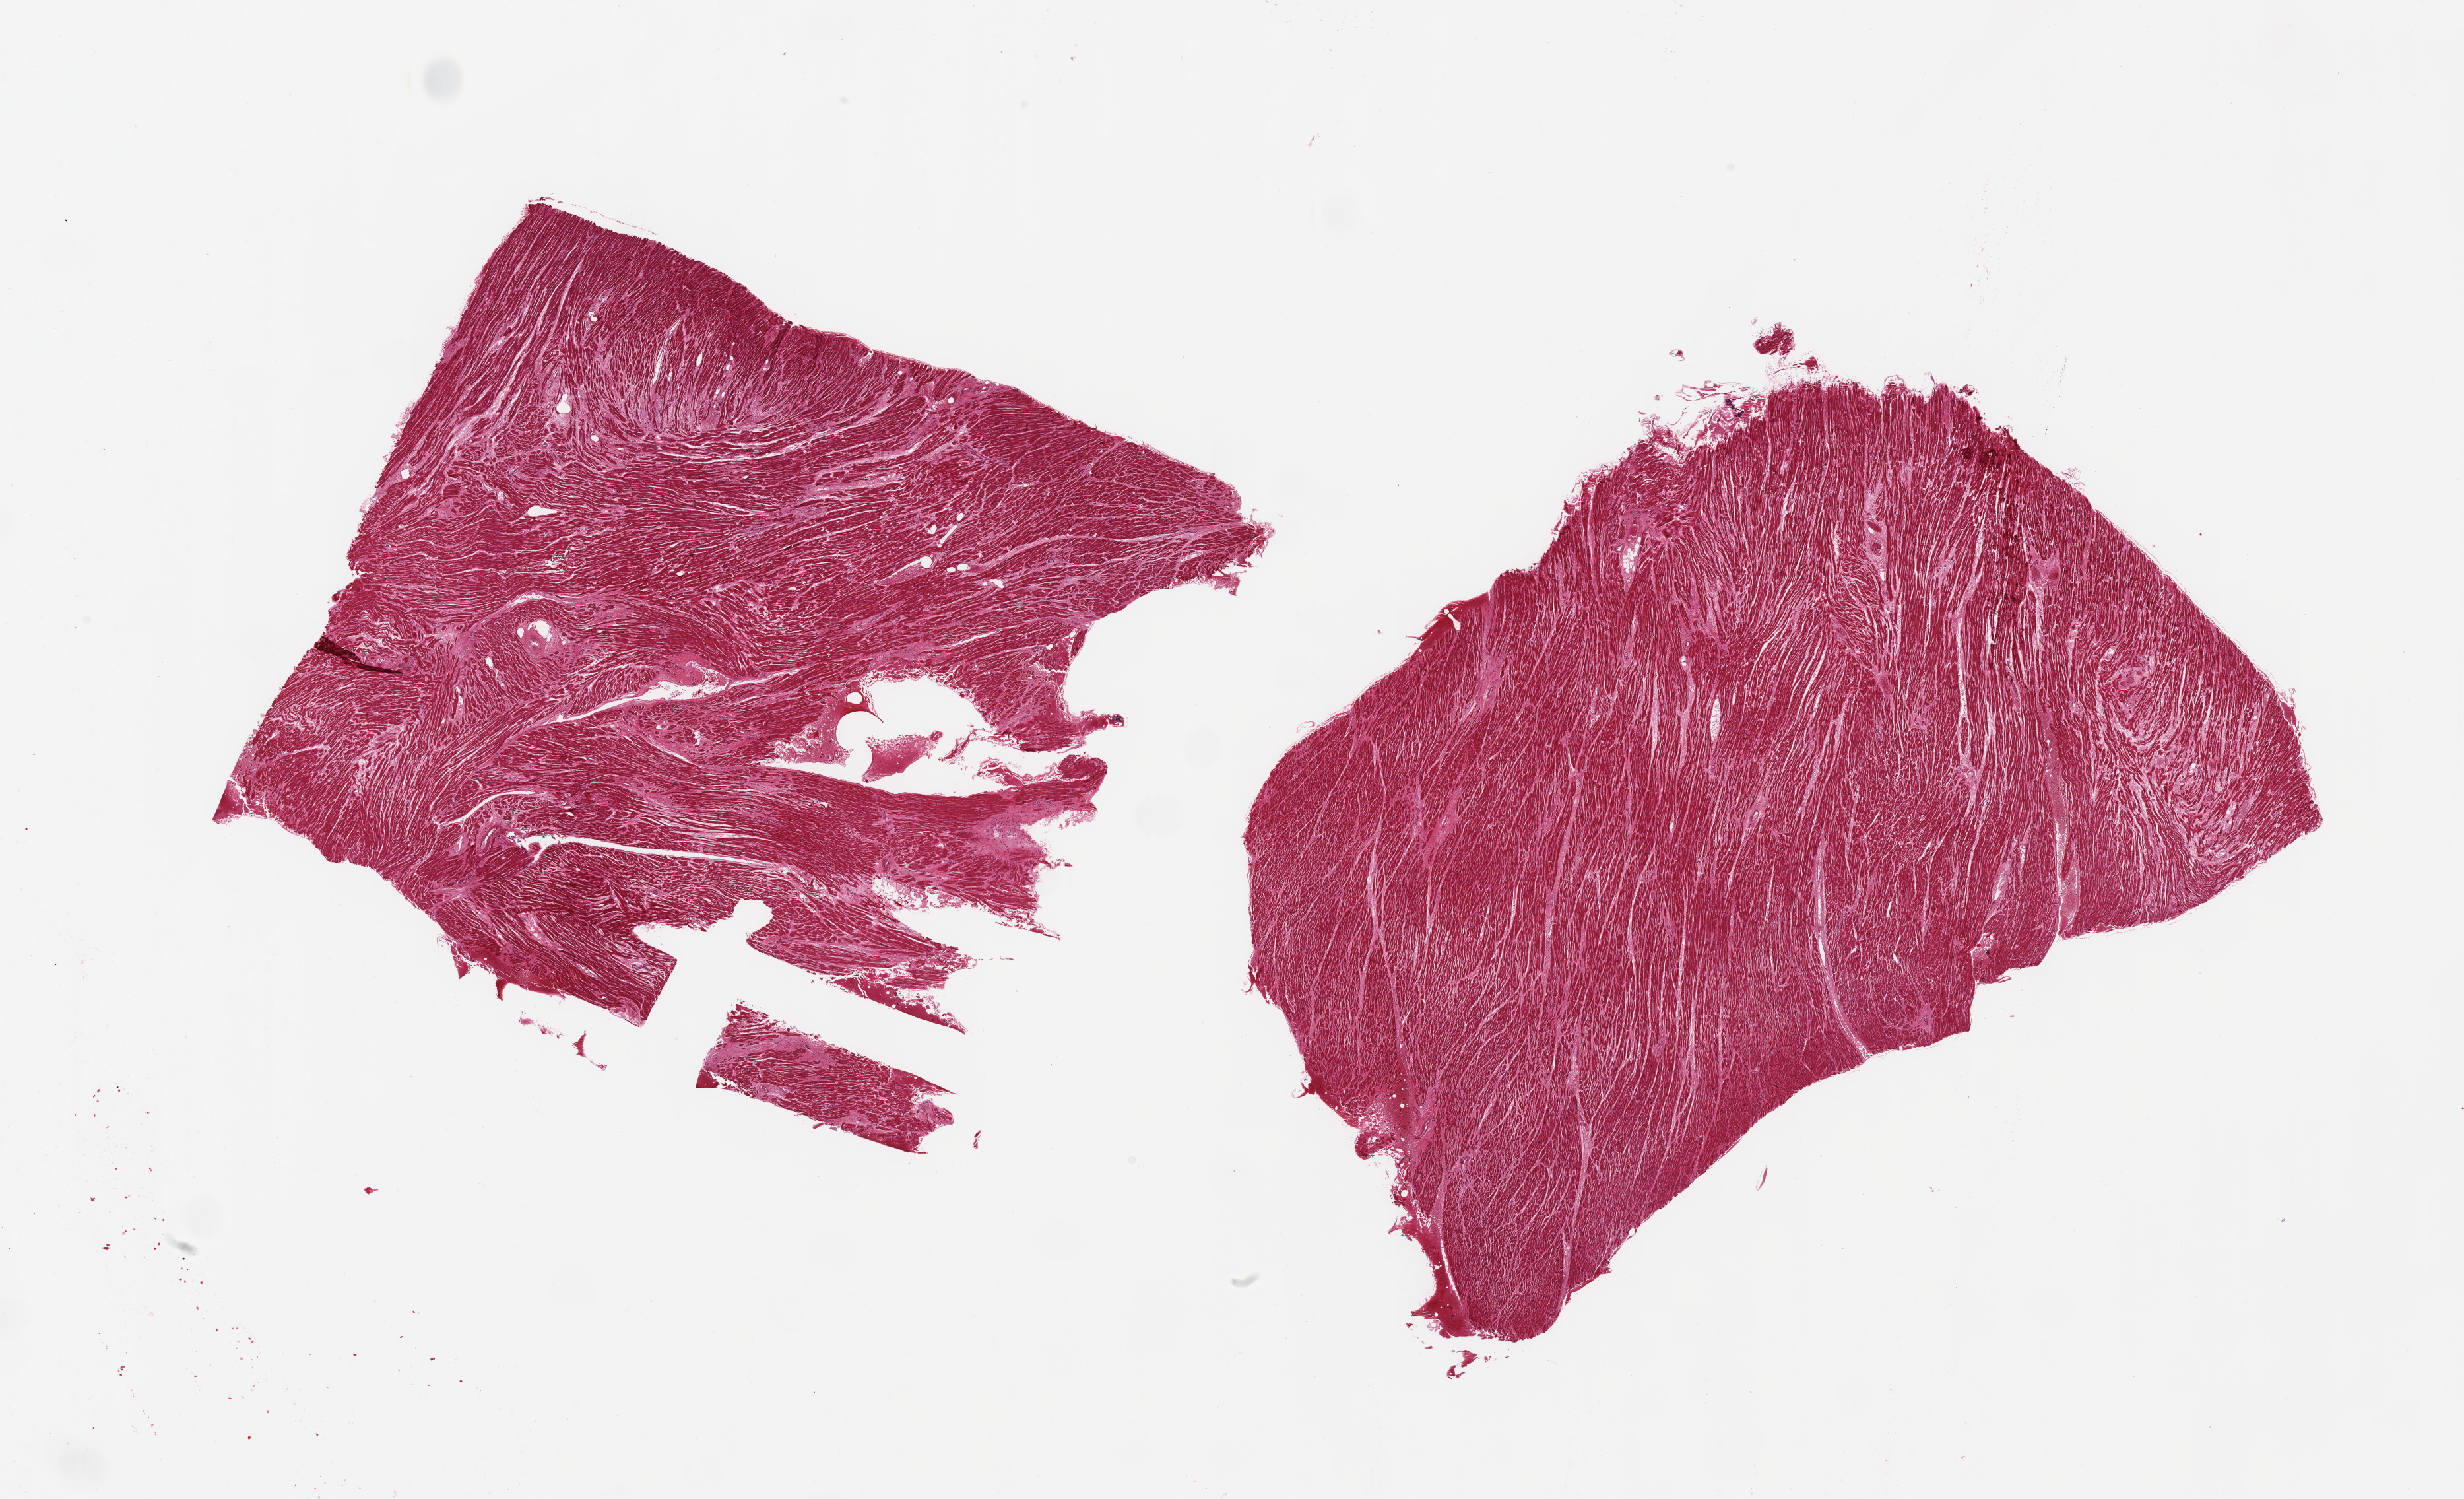
Digitized hematoxylin and eosin (H&E)-stained section, brightfield, a low-resolution overview of the entire scanned area, about 29.5 x 18.0 mm (acquisition: 20x scan); PAXgene-fixed, paraffin-embedded tissue; target tissue: auricular appendage; donor tissue sample. Donor sex: male.
Pathologist's review note for this sample: 2 pieces; interstitial and patchy fibrosis.